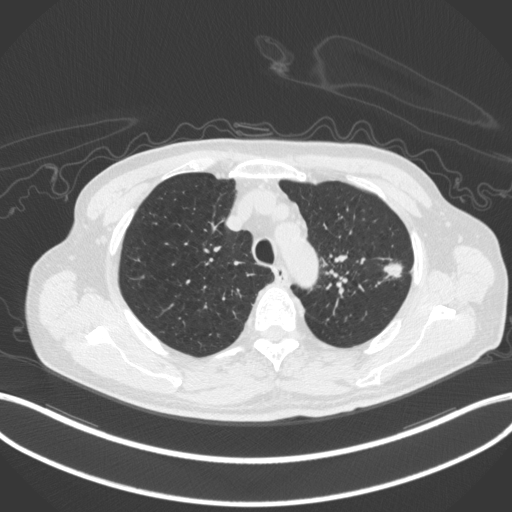
Chest CT, one axial slice. Position 348 of 420 along the scan axis. Lung window (W 1500 / L -600 HU). 1 mm slice thickness. 512 × 512 image matrix, field of view 400 × 400 mm. Patient: male, 77 years. From the clinical record (not read from this slice): clinical TNM (as recorded): T3 N1 M0.
Annotated regions visible in this slice (bounding box drawn by a radiologist):
- lung tumour (recorded histology: adenocarcinoma): bounding box (x1, y1, x2, y2) in pixels: (380, 258, 405, 280)